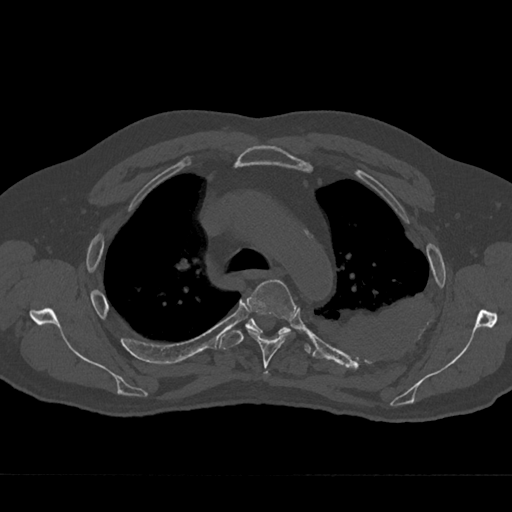
CT including the spine, one axial slice. Slice 504 of 797 in the series (ordered by position). Reconstruction kernel Br40s/3. 120 kVp. Bone window (W 1800 / L 400 HU). 0.5 mm slice thickness. 512 × 512 image matrix. Patient: male, 75 years. Case-level facts recorded for this patient, not image findings: primary cancer: renal.
Annotated regions visible in this slice (semi-automatically segmented with operator editing):
- T4 vertebra: bounding box (x1, y1, x2, y2) in pixels: (246, 279, 295, 376)
- T5 vertebra: (219, 319, 311, 354)